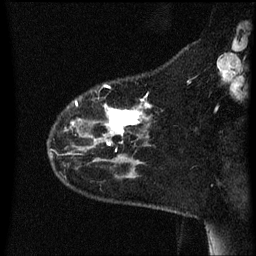
Breast MRI (dynamic contrast-enhanced), one sagittal slice; position 13 of 60 along the scan axis; dynamic contrast-enhanced series, image 2 of 3 at this slice position (ordered by acquisition); 1.5 T; TE 4.2 ms, TR 8.4 ms; 2.2 mm slice thickness; 256 × 256 image matrix. Patient: female, 35 years. Case-level facts recorded for this patient, not image findings: setting: breast cancer imaged before/during neoadjuvant chemotherapy; receptor status: HER2-positive.
Annotated regions visible in this slice (semi-automatically segmented with operator editing):
- analysis volume of interest (the breast-tissue region the enhancement analysis was run in; not a lesion): bounding box [x1, y1, x2, y2] px = [50, 84, 152, 163]
- tumour enhancement mask (voxels above the 70 % enhancement threshold inside the analysis volume of interest): [73, 100, 152, 135]